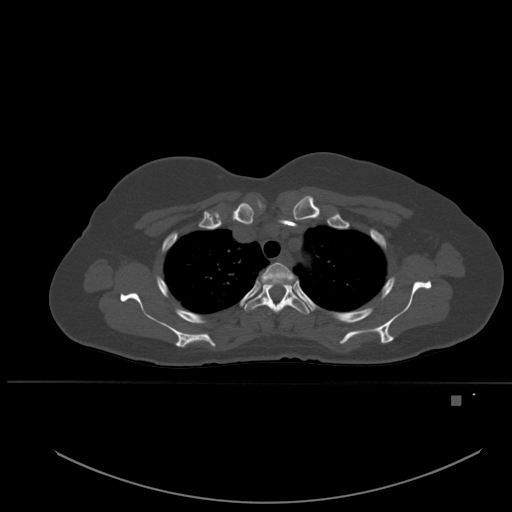
CT including the spine, one axial slice. Position 397 of 651 along the scan axis. Bone window (W 1800 / L 400 HU). 512 × 512 image matrix, field of view 443 × 443 mm. Female patient, age 49 years. Case-level facts recorded for this patient, not image findings: primary cancer: breast; vertebrae with lytic lesions (as recorded): L3, T12, L4.
Outlined on this slice (semi-automatically segmented with operator editing):
- T2 vertebra: bounding box <261,262,296,283> (left, top, right, bottom; pixels)
- T3 vertebra: <244,282,310,315>